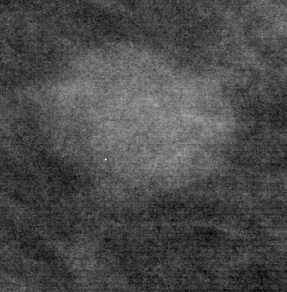
Cropped region of a digitized screen-film mammogram centred on a radiologist-marked abnormality; right breast; CC view; BI-RADS breast density category 1 (scale 1–4).
Finding: mass, shape round, margins circumscribed; BI-RADS assessment category 2; pathology result (as recorded, not read from the image): benign.